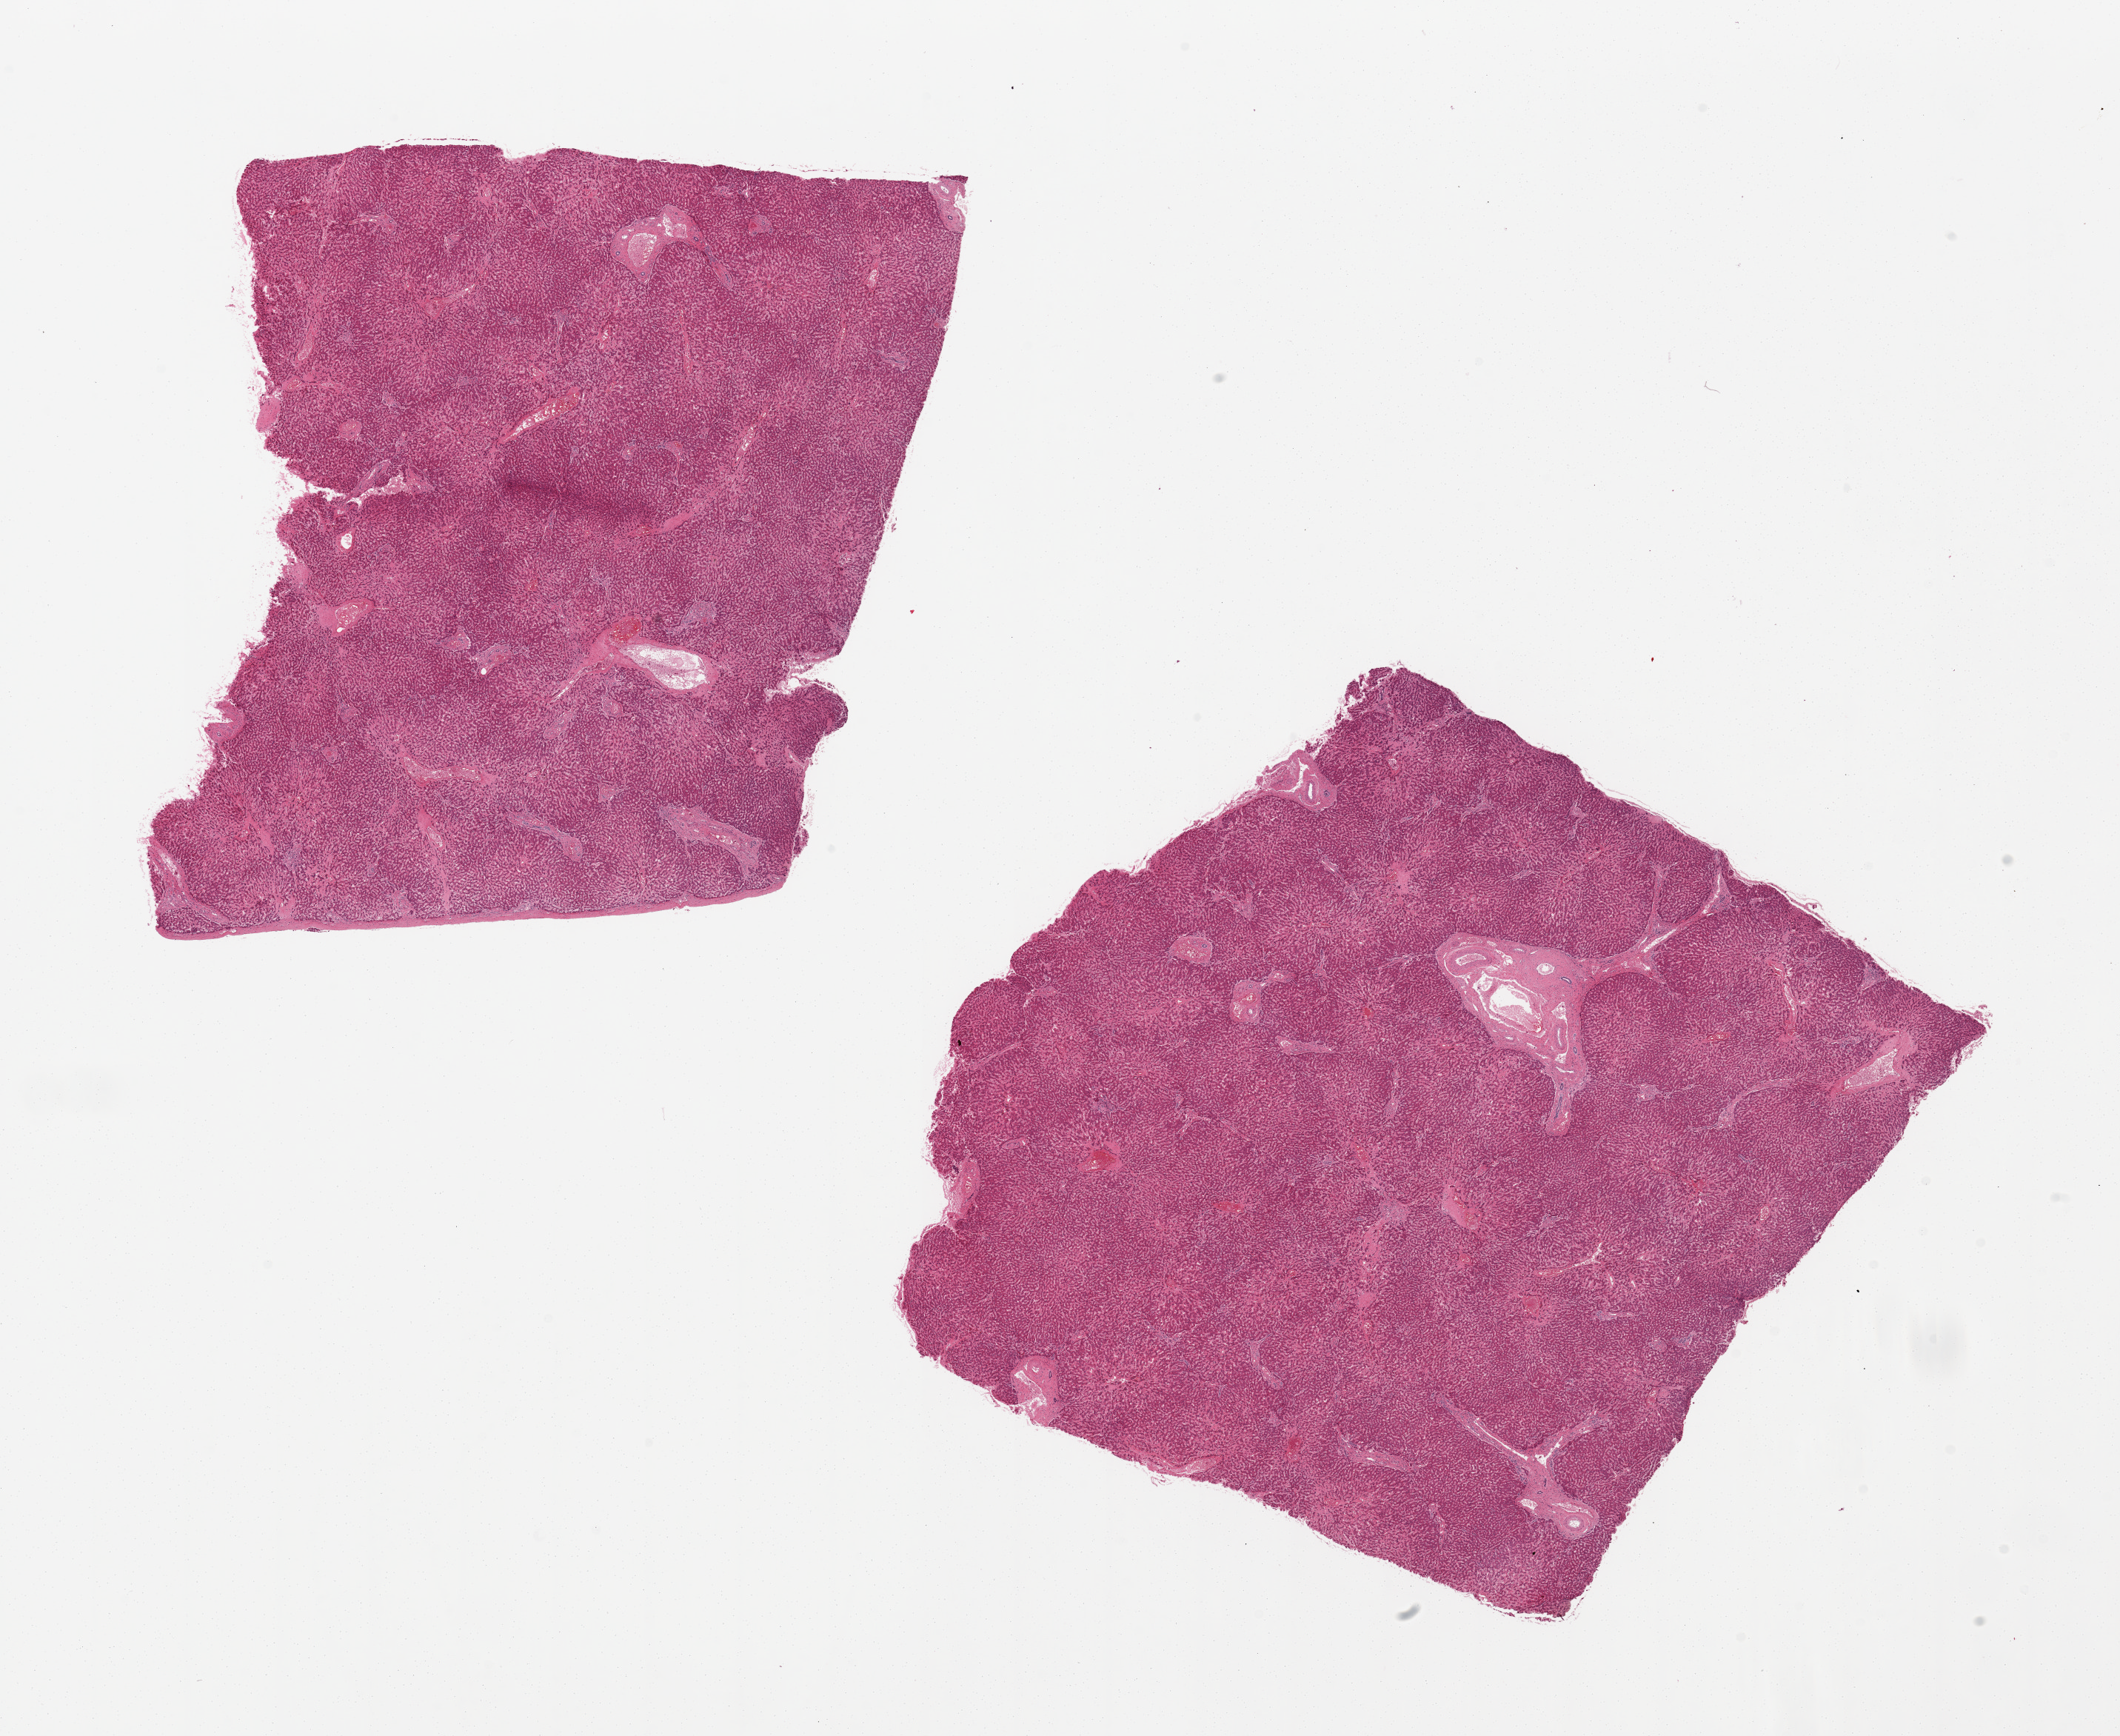
Whole-slide image, haematoxylin and eosin stain, brightfield — a low-resolution overview of the entire scanned area, about 22.6 x 18.5 mm (slide scanned at 20x), PAXgene-fixed, paraffin-embedded tissue, section of liver (target tissue), donor tissue sample. Donor sex: male.
• reviewer comment on this tissue sample: 2 pieces